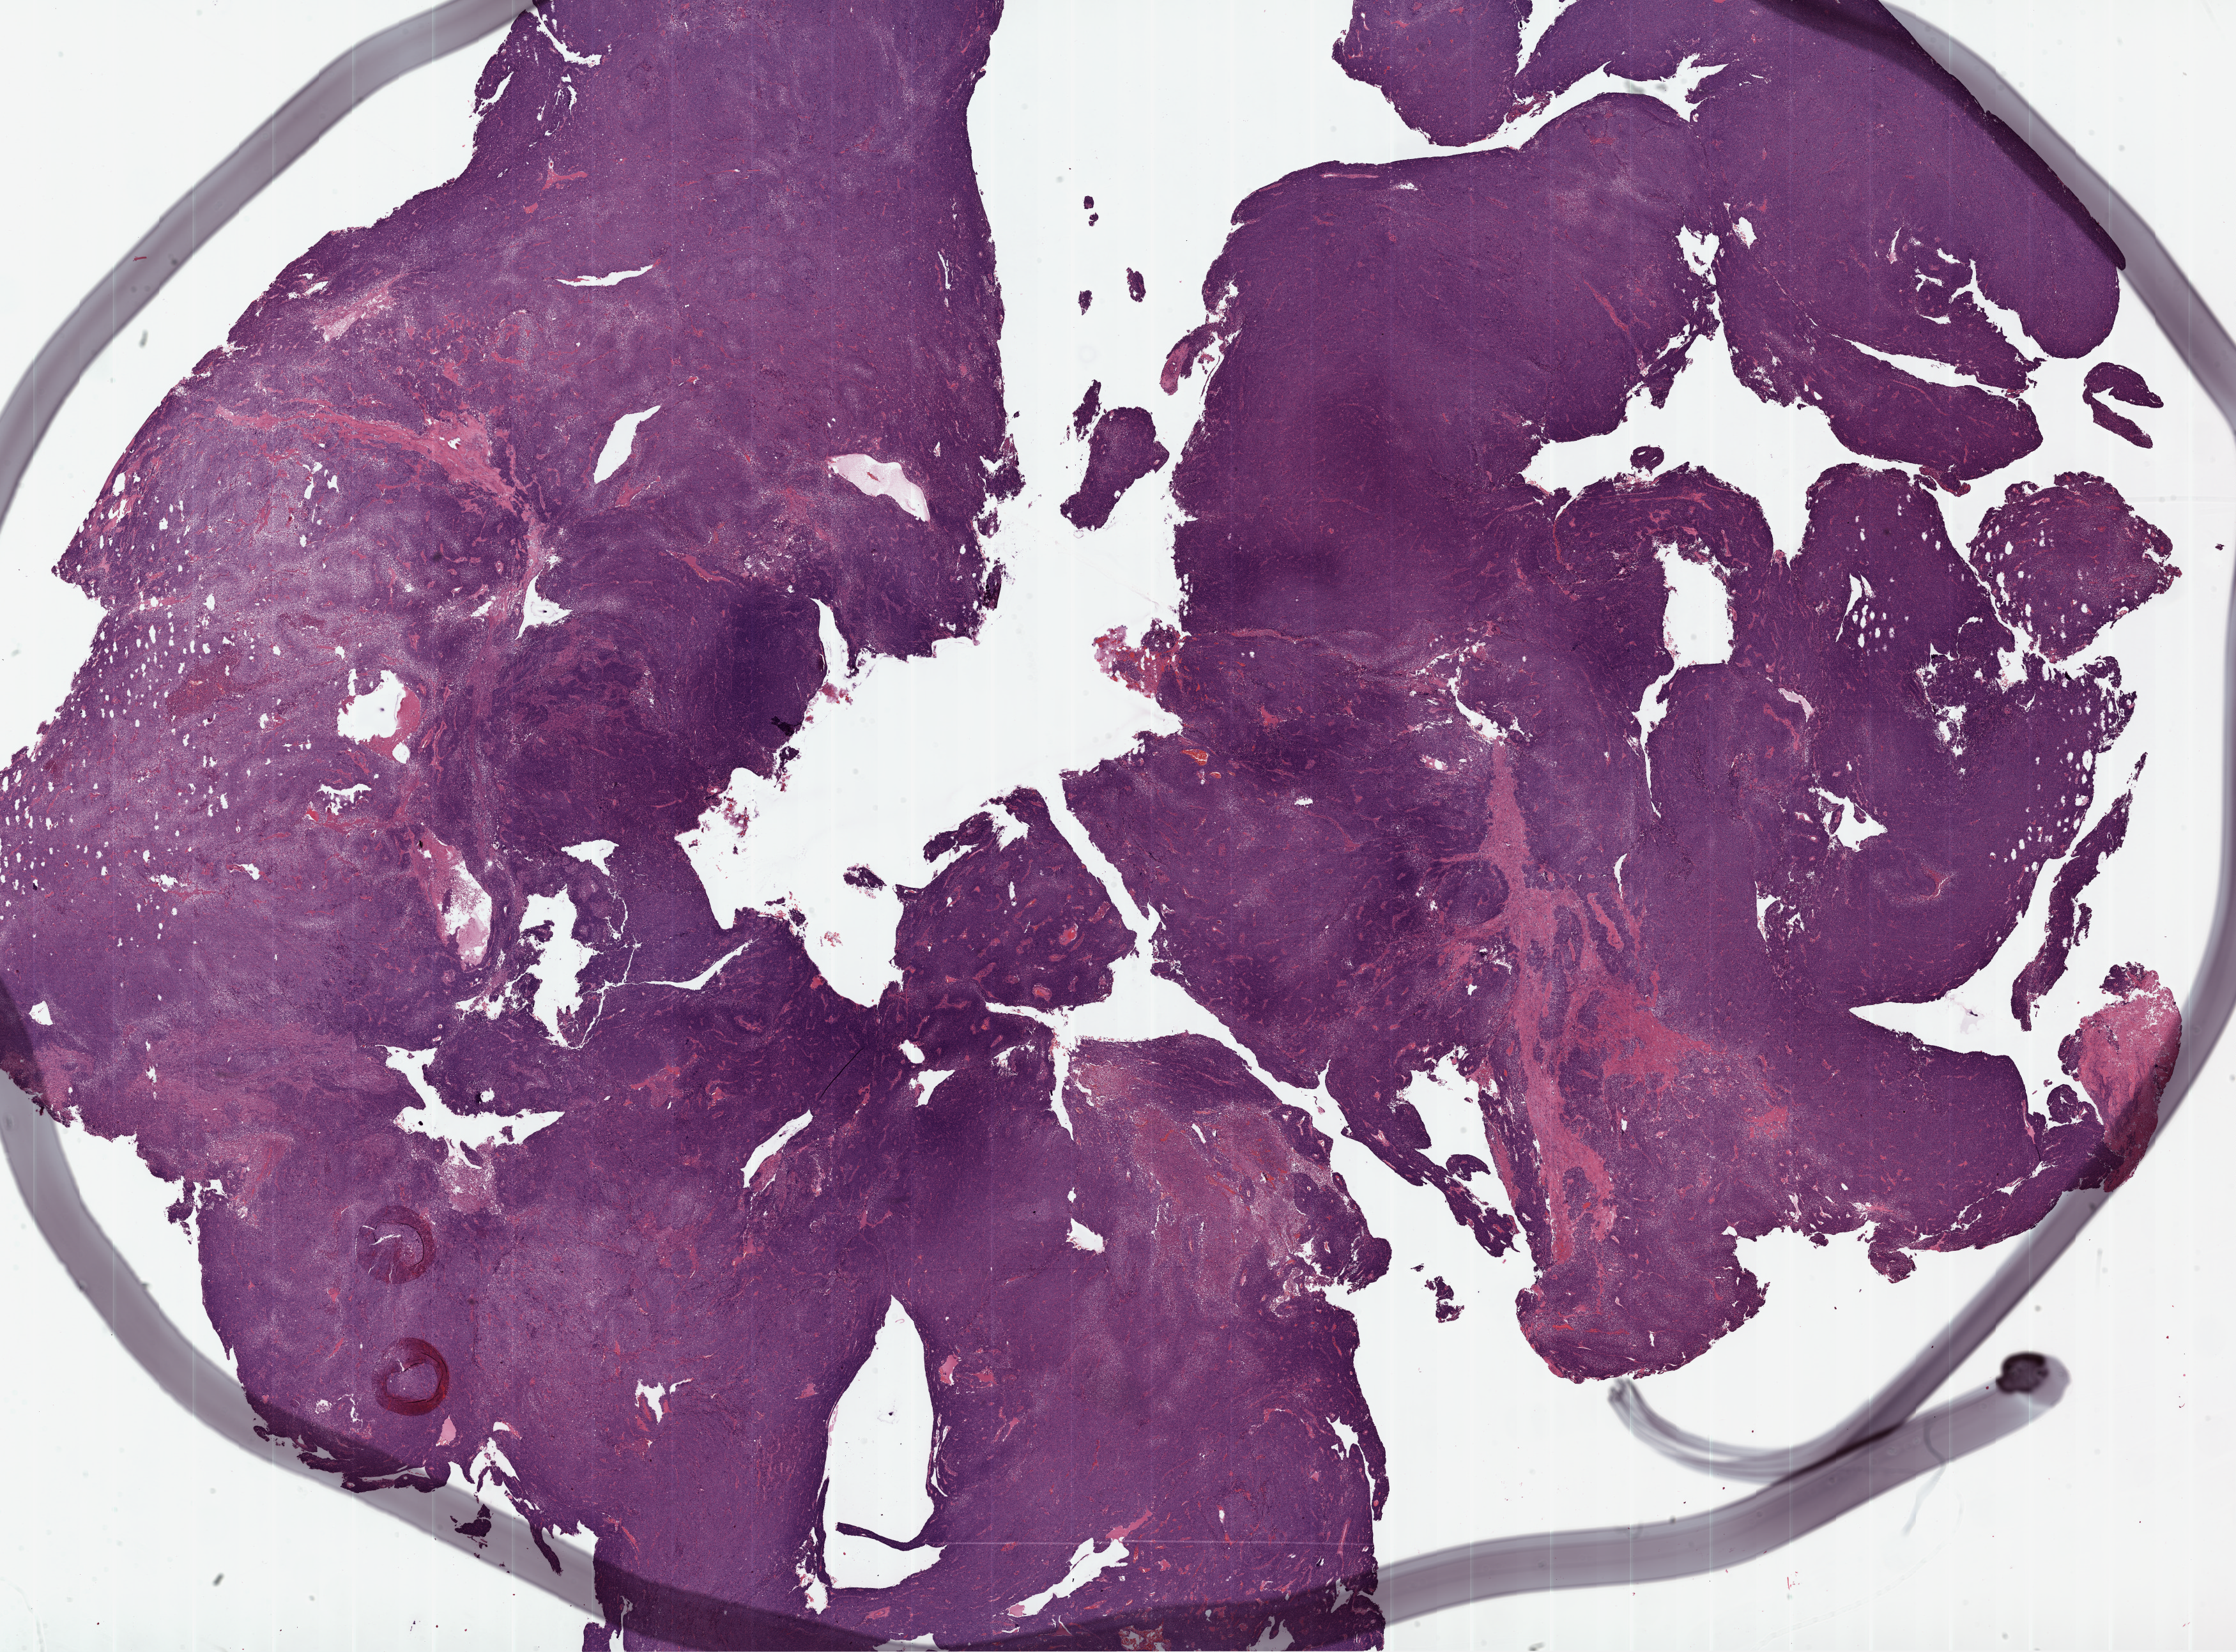
Digitized H&E tissue section (whole slide), whole scanned area (about 28.1 x 20.8 mm, slide scanned at 20x) shown as a low-resolution overview; frozen section; sample: primary tumour, ovary. Female patient; age at initial diagnosis 61 years. Histologic grade: G3 (poorly differentiated). Slide review estimates, as recorded: tumour cells 85%, tumour nuclei 90%, normal cells 0%, stromal cells 10%, necrosis 5%.
FIGO stage: IIIC. Diagnosis: Serous cystadenocarcinoma, NOS.